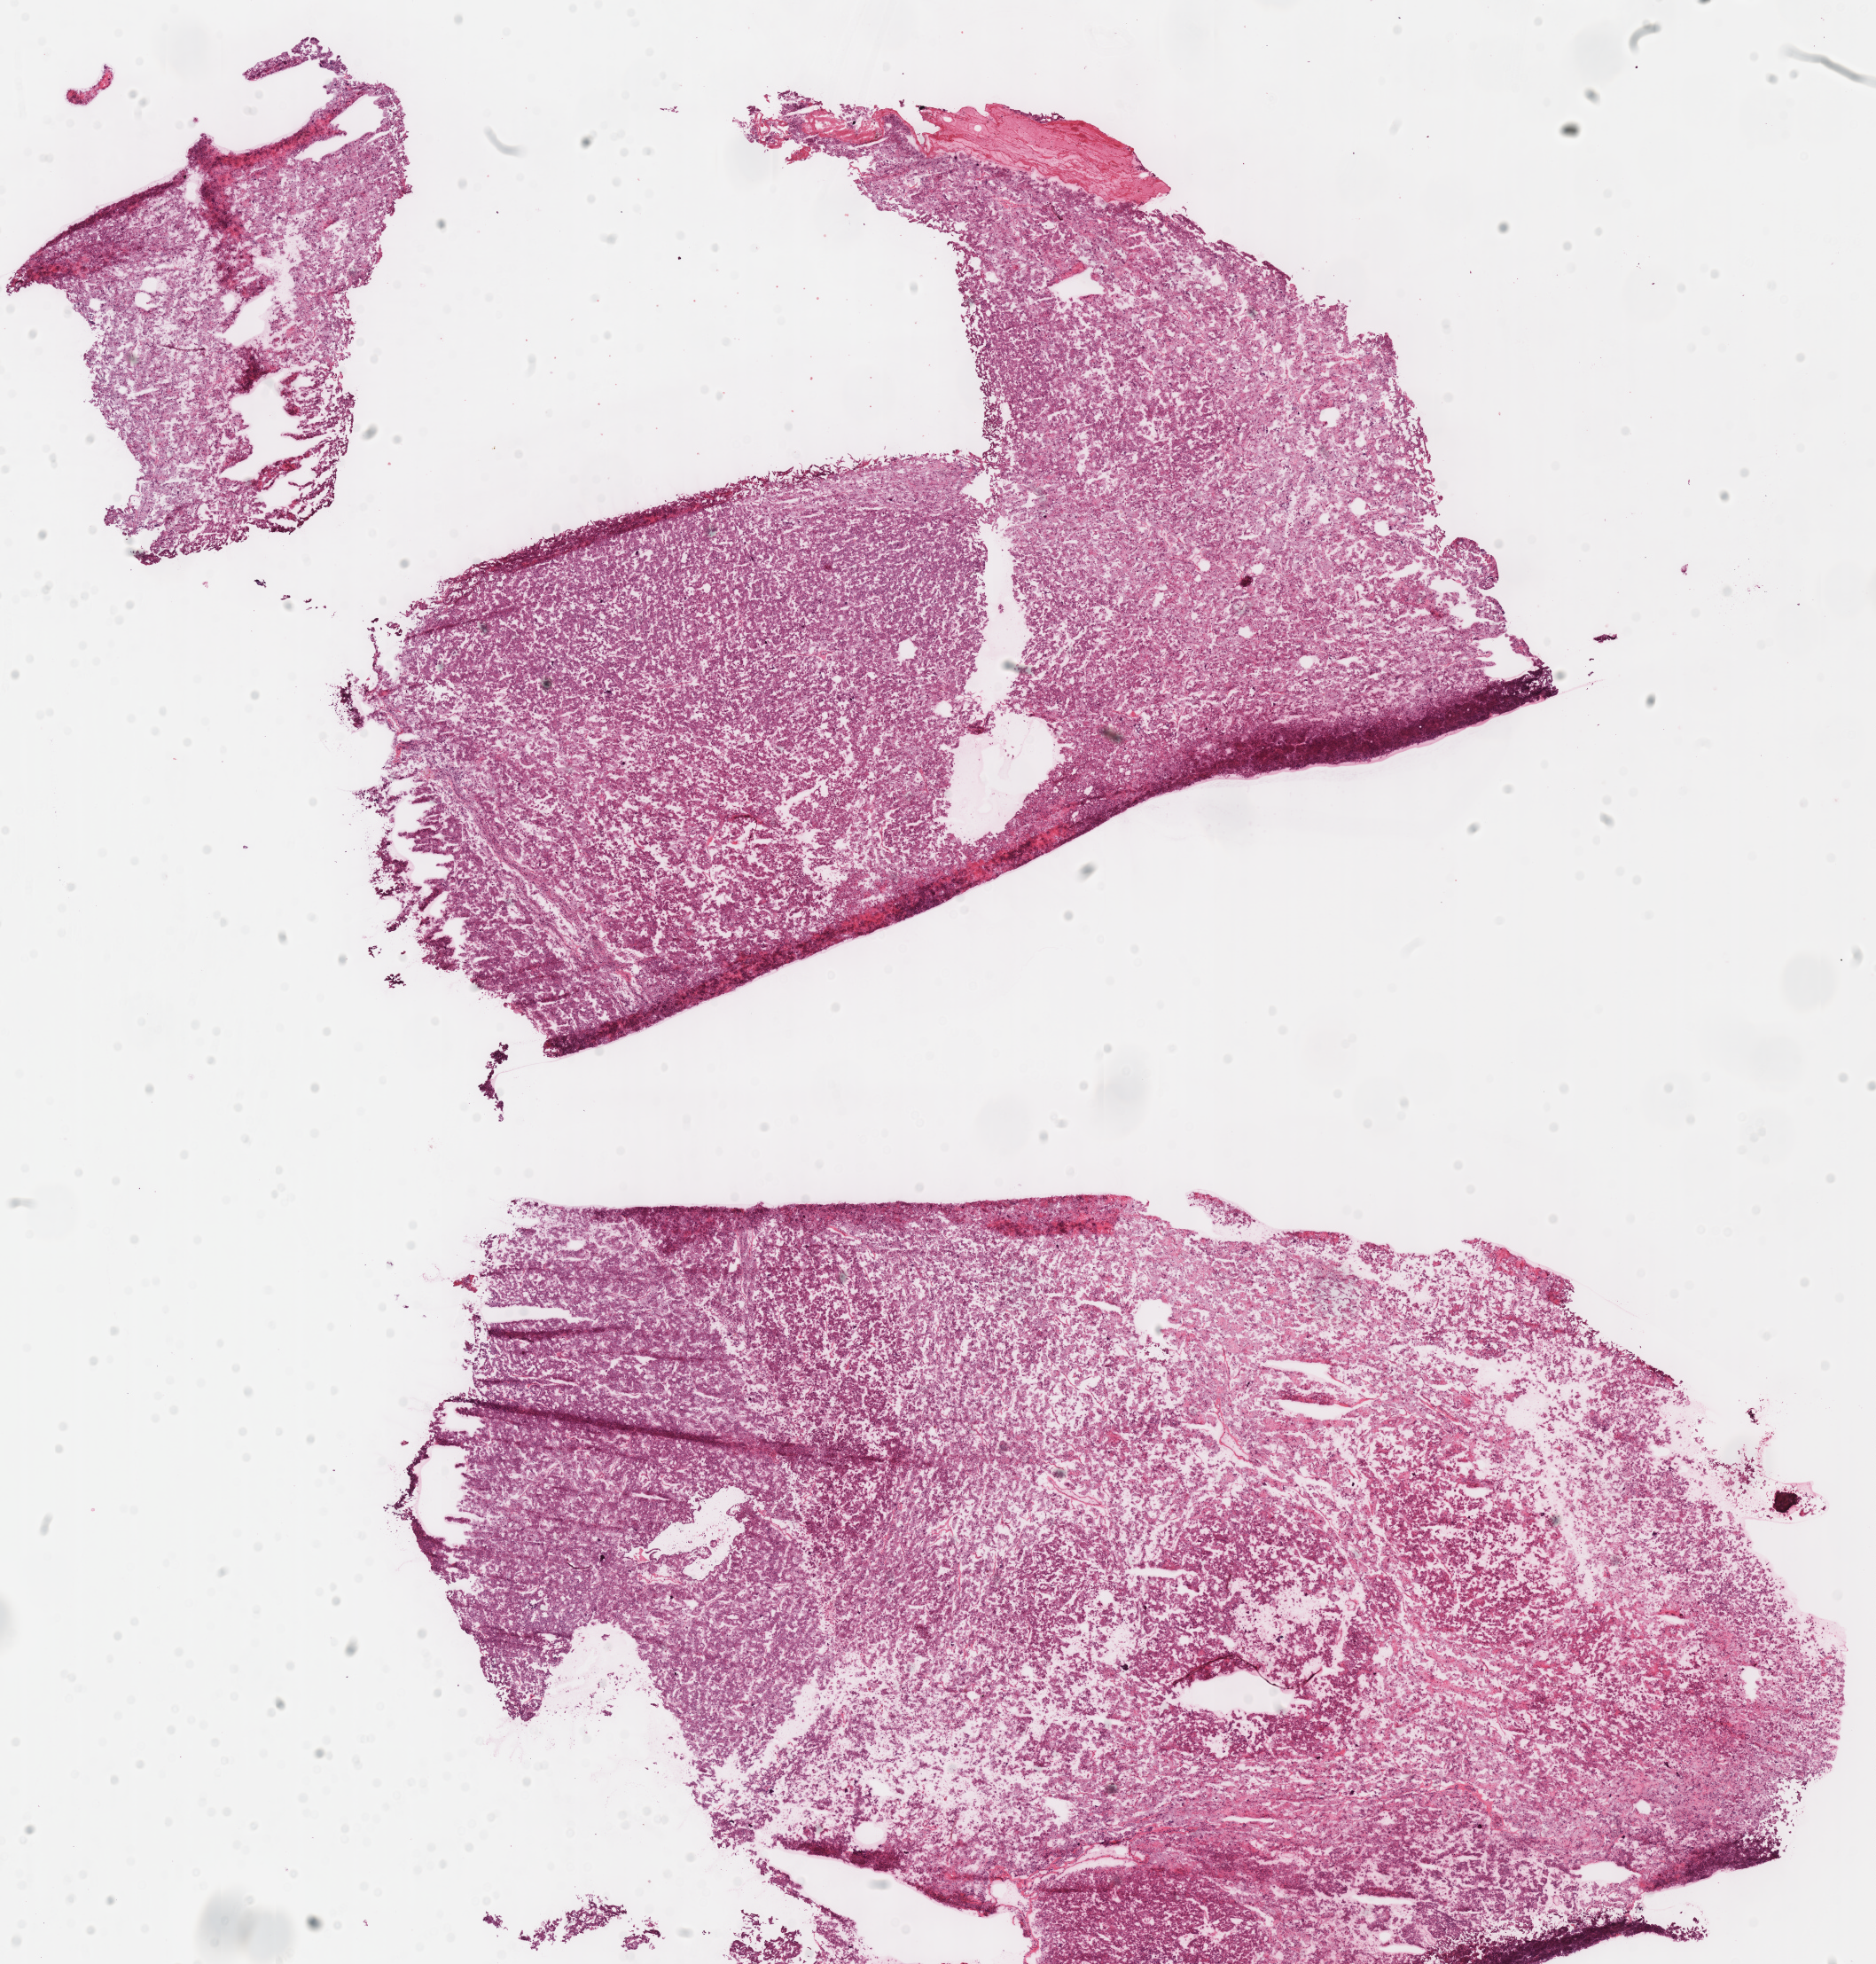
Whole-slide histology image, H&E-stained — whole scanned area (about 16.6 x 17.4 mm, acquisition: 40x scan) shown as a low-resolution overview, frozen section from the top of the tissue portion, primary tumour sample from the kidney. Male patient; age at initial diagnosis 26 years. Slide review estimates, as recorded: tumour cells 95%, tumour nuclei 95%, normal cells 0%, stromal cells 5%, necrosis 0%.
Pathologic diagnosis: Renal cell carcinoma, chromophobe type. Lymph nodes positive (case pathology): 0 of 1 examined. Laterality: right. AJCC pathologic stage: II.